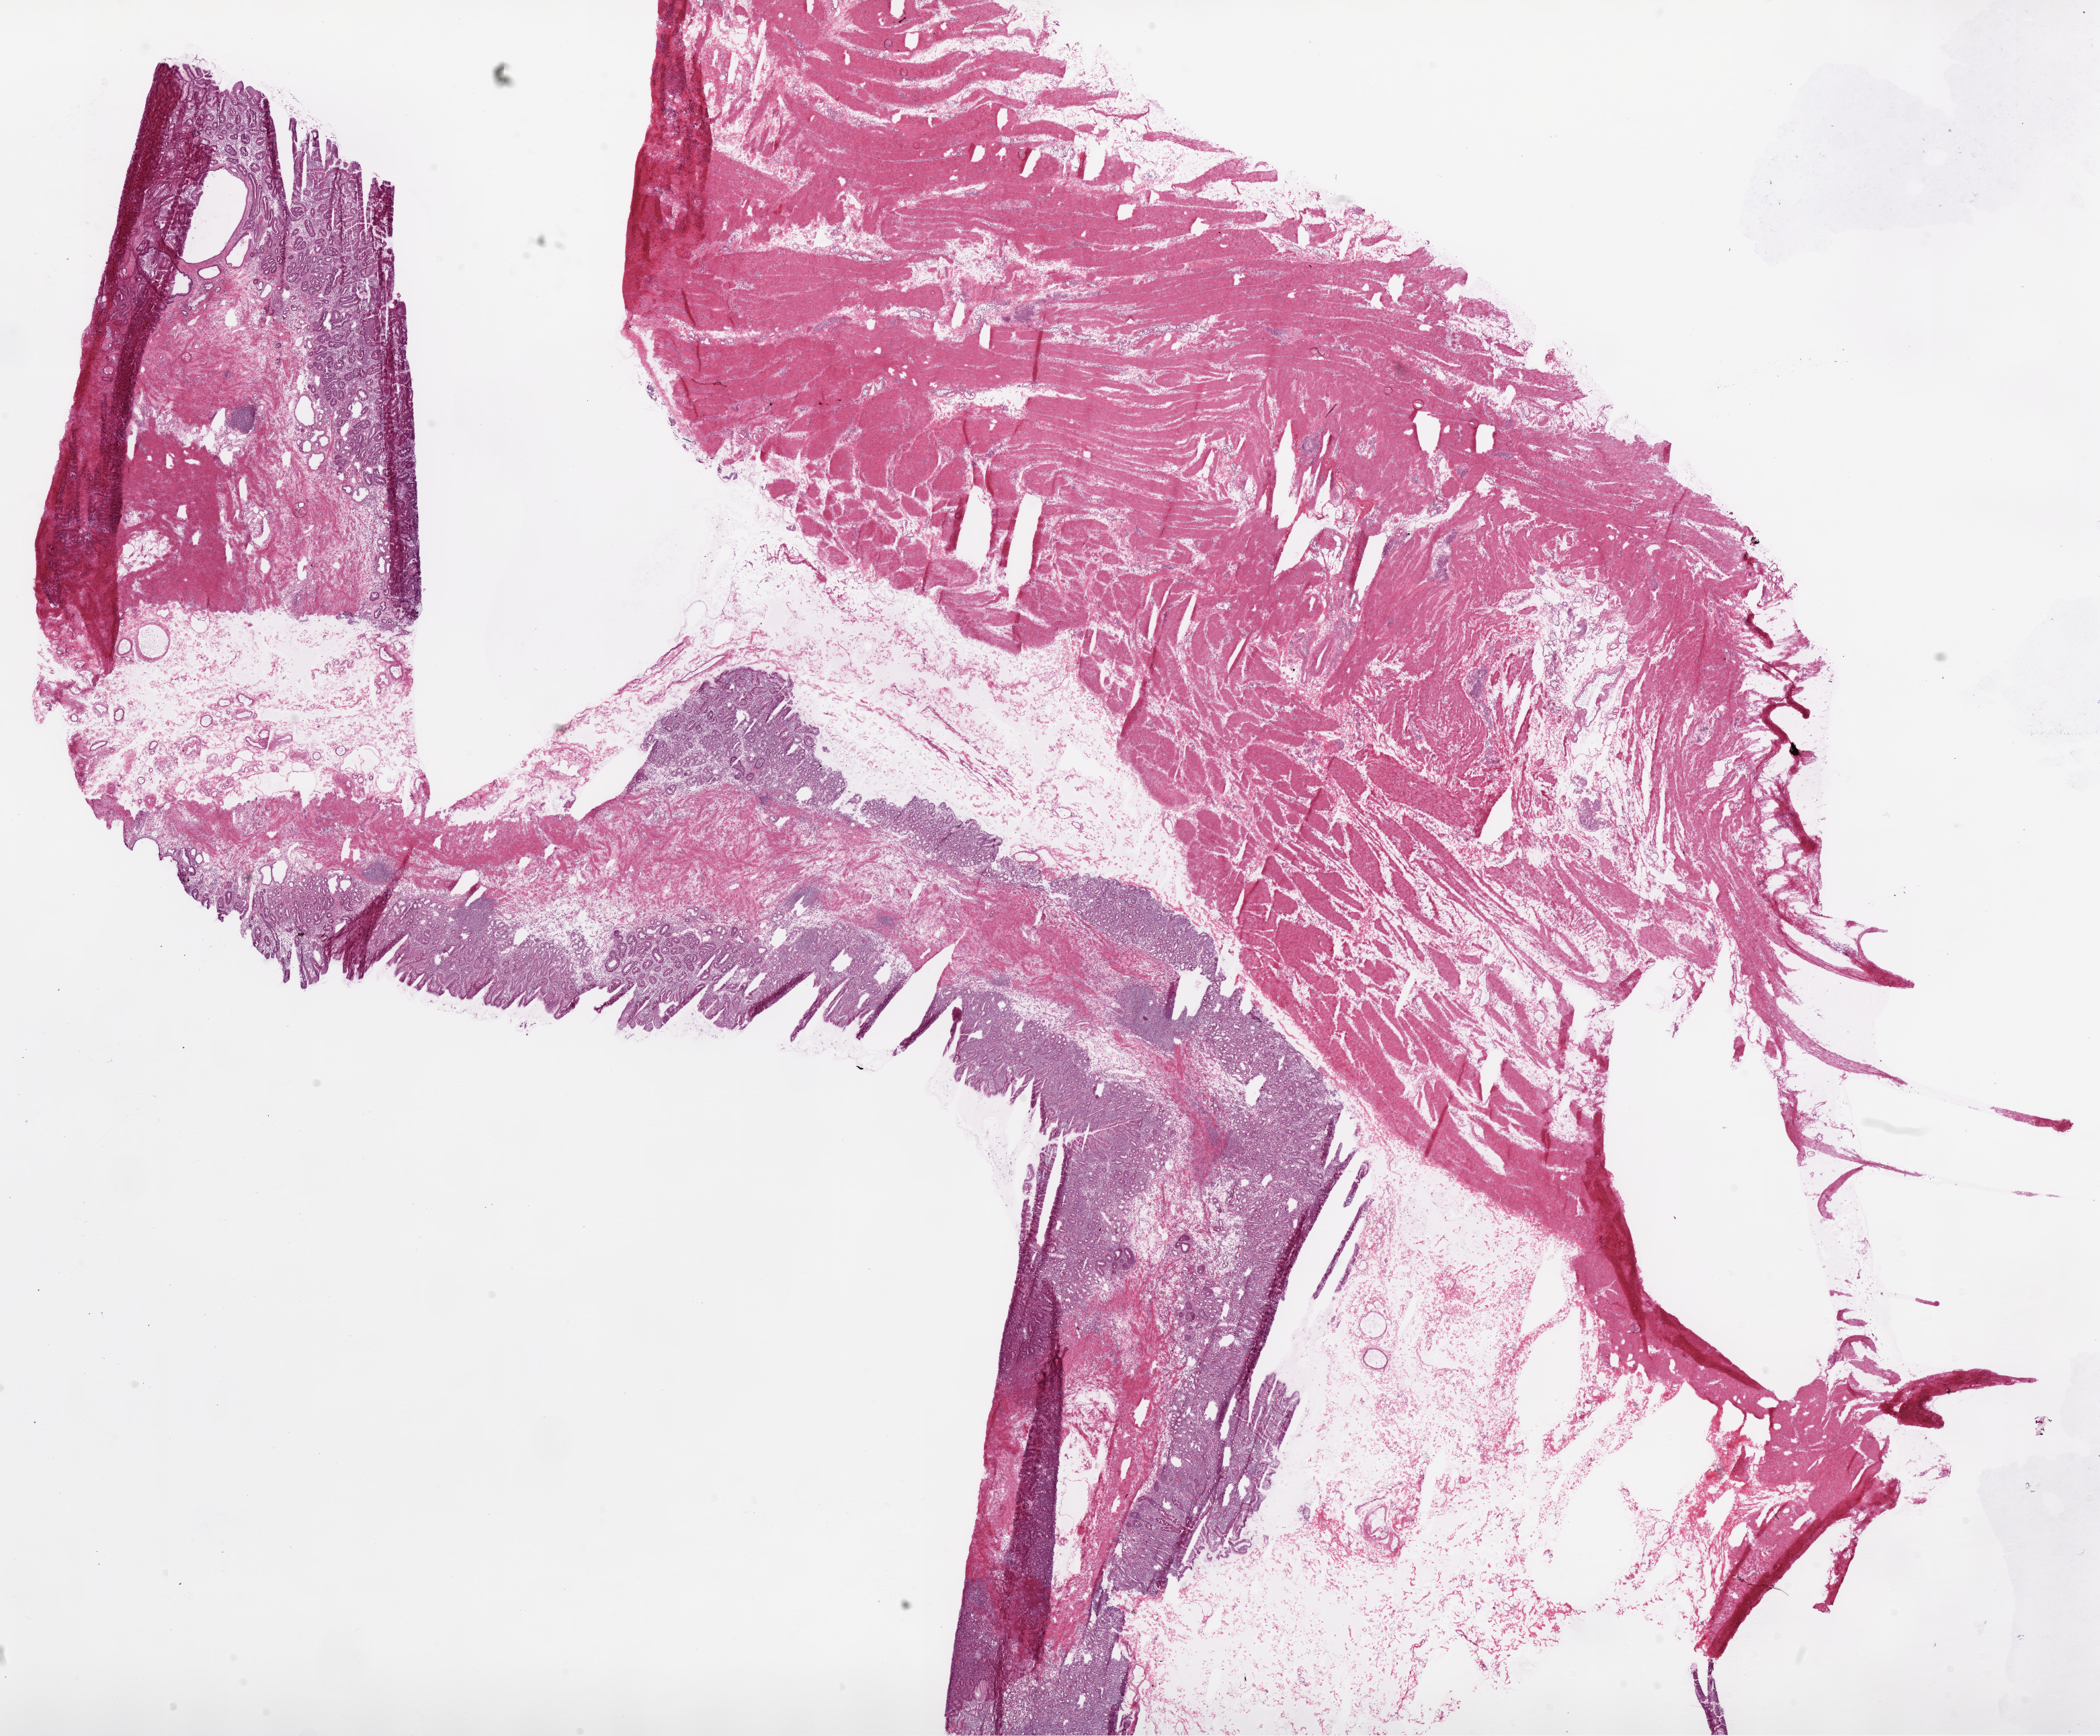
Whole-slide histology image, H&E, shown as a low-resolution overview of the whole scanned area (about 25.1 x 20.7 mm); frozen section; sample: solid tissue normal (non-tumour tissue), stomach. Patient: female, age at initial diagnosis 80 years.
This section: solid tissue normal (non-tumour) sample from the same patient. Patient diagnosis: Adenocarcinoma, NOS.